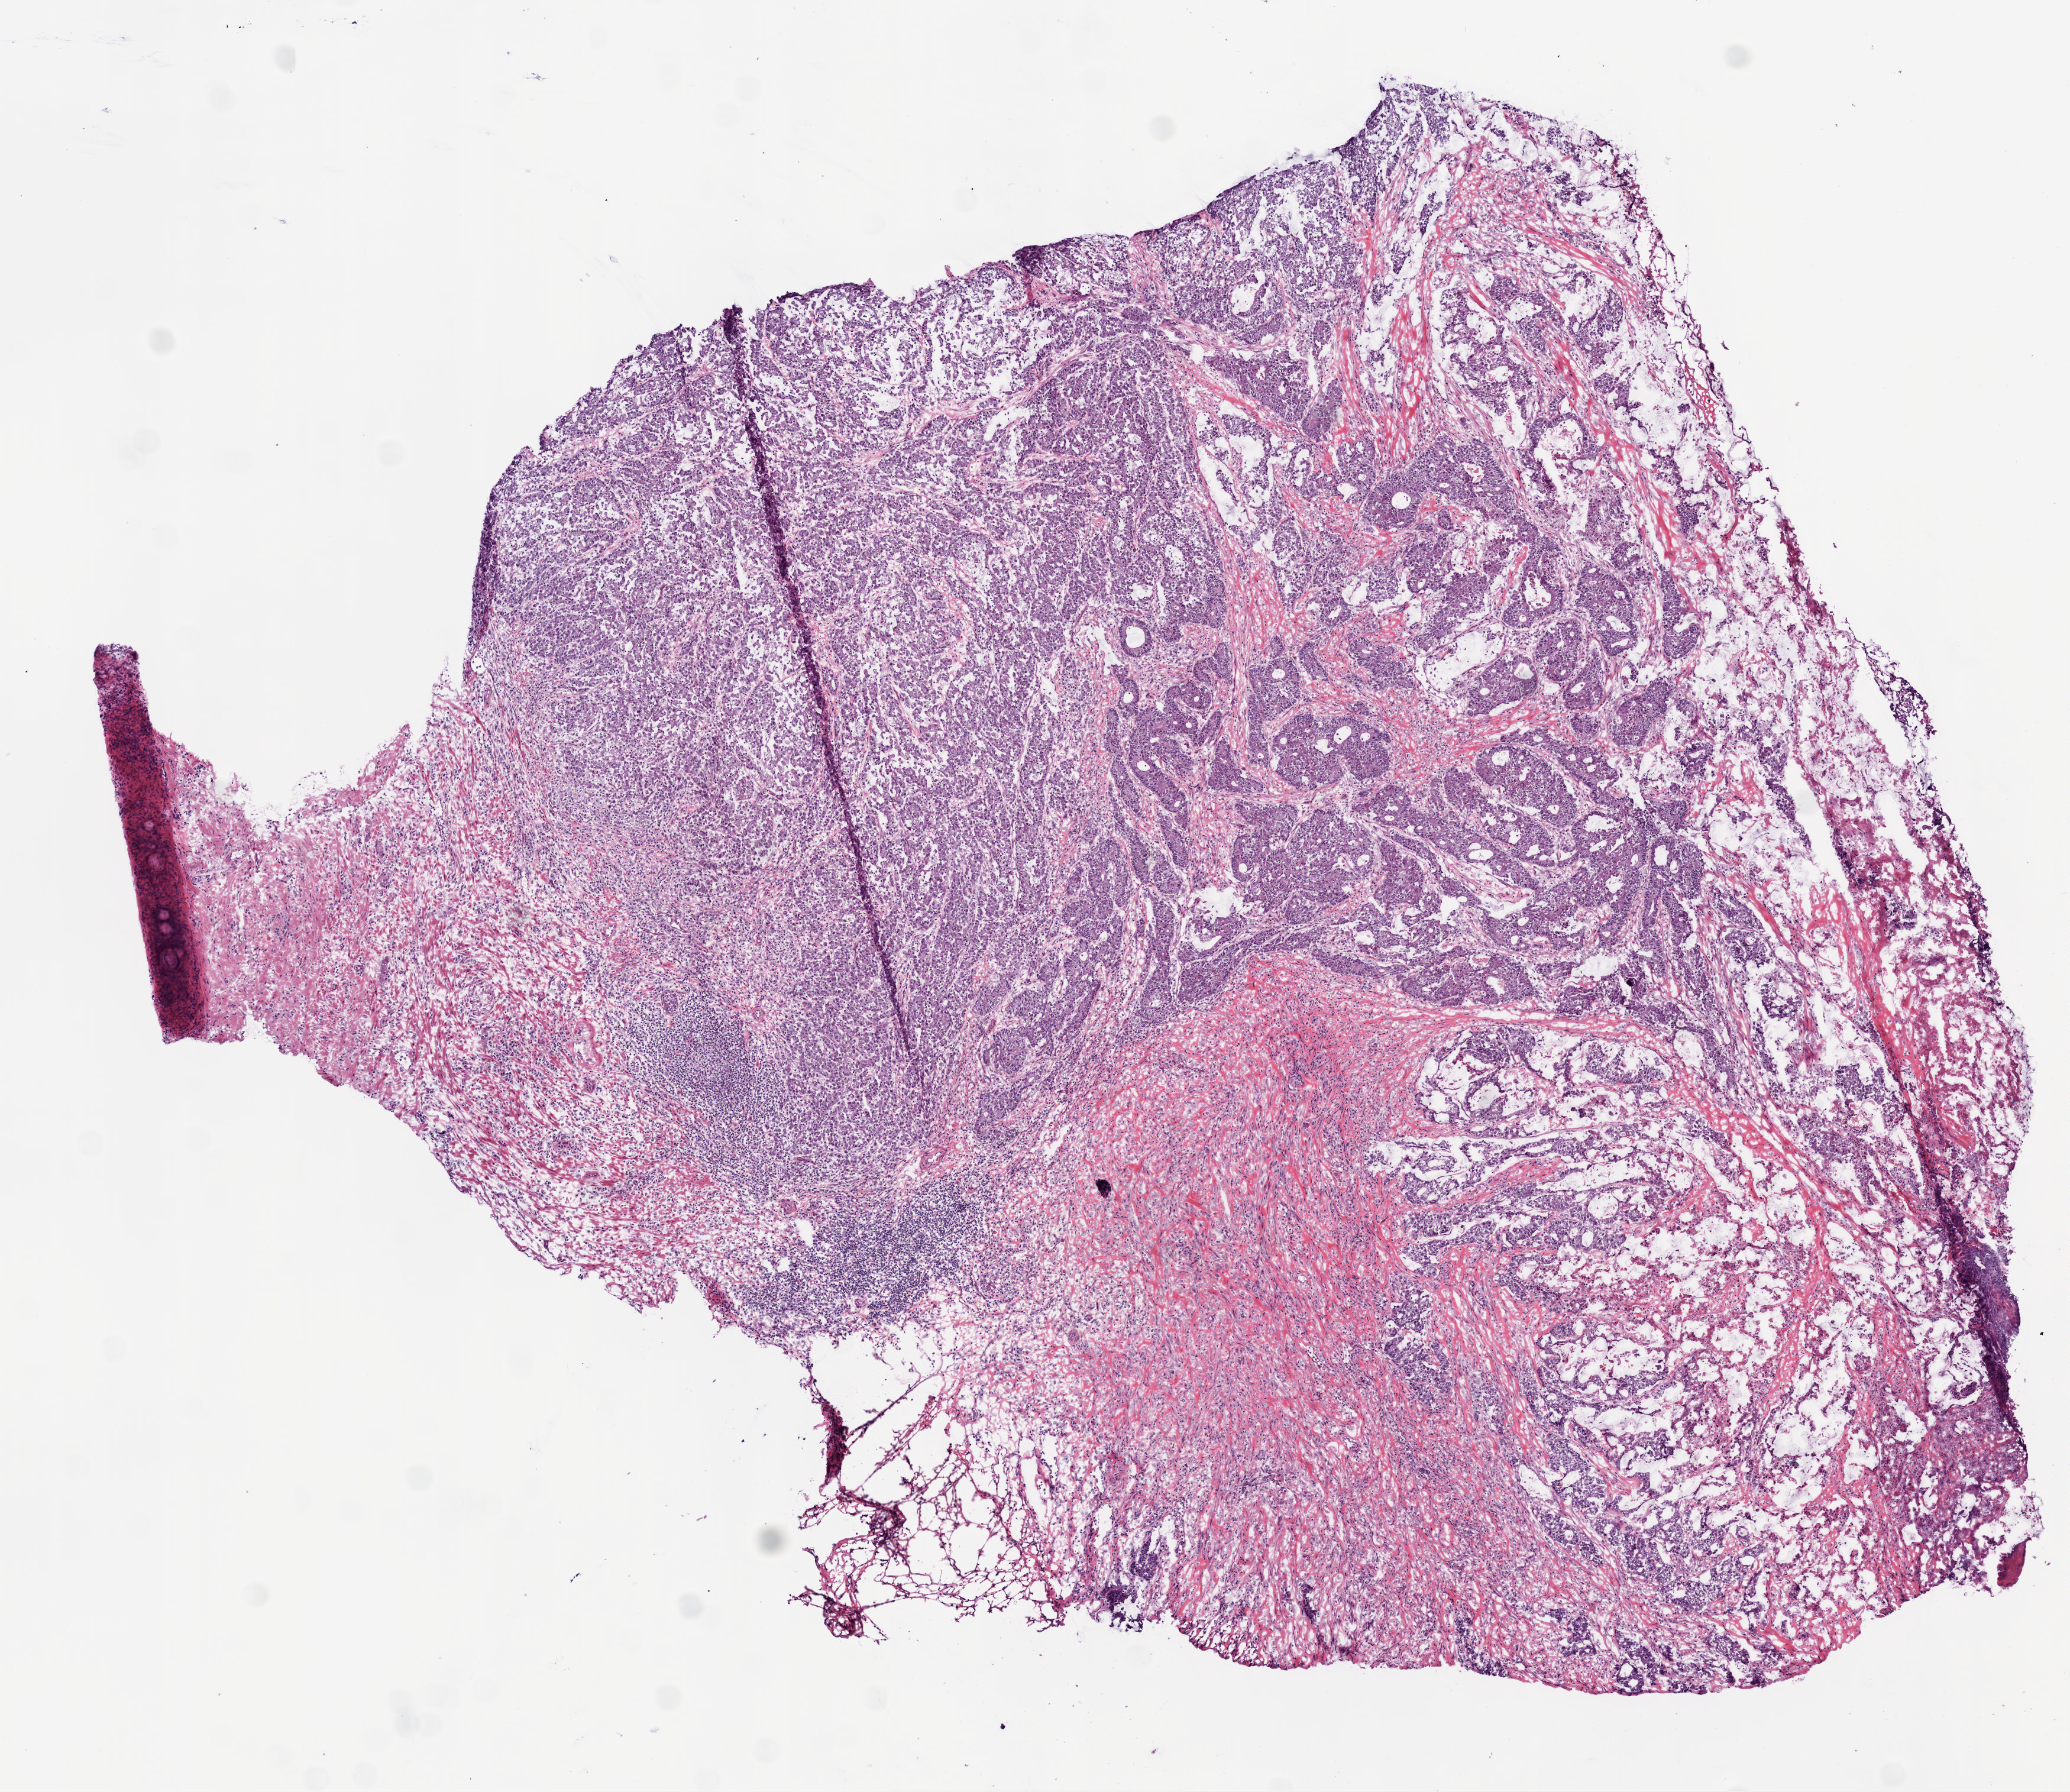
H&E whole-slide image — whole scanned area (about 7.0 x 6.1 mm, from a 20x scan) shown as a low-resolution overview, frozen section, primary tumour sample from the colon. Female patient. Composition of this section per pathologist review: tumour cells 65%, tumour nuclei 75%.
Histologic diagnosis: Mucinous adenocarcinoma (ascending colon).